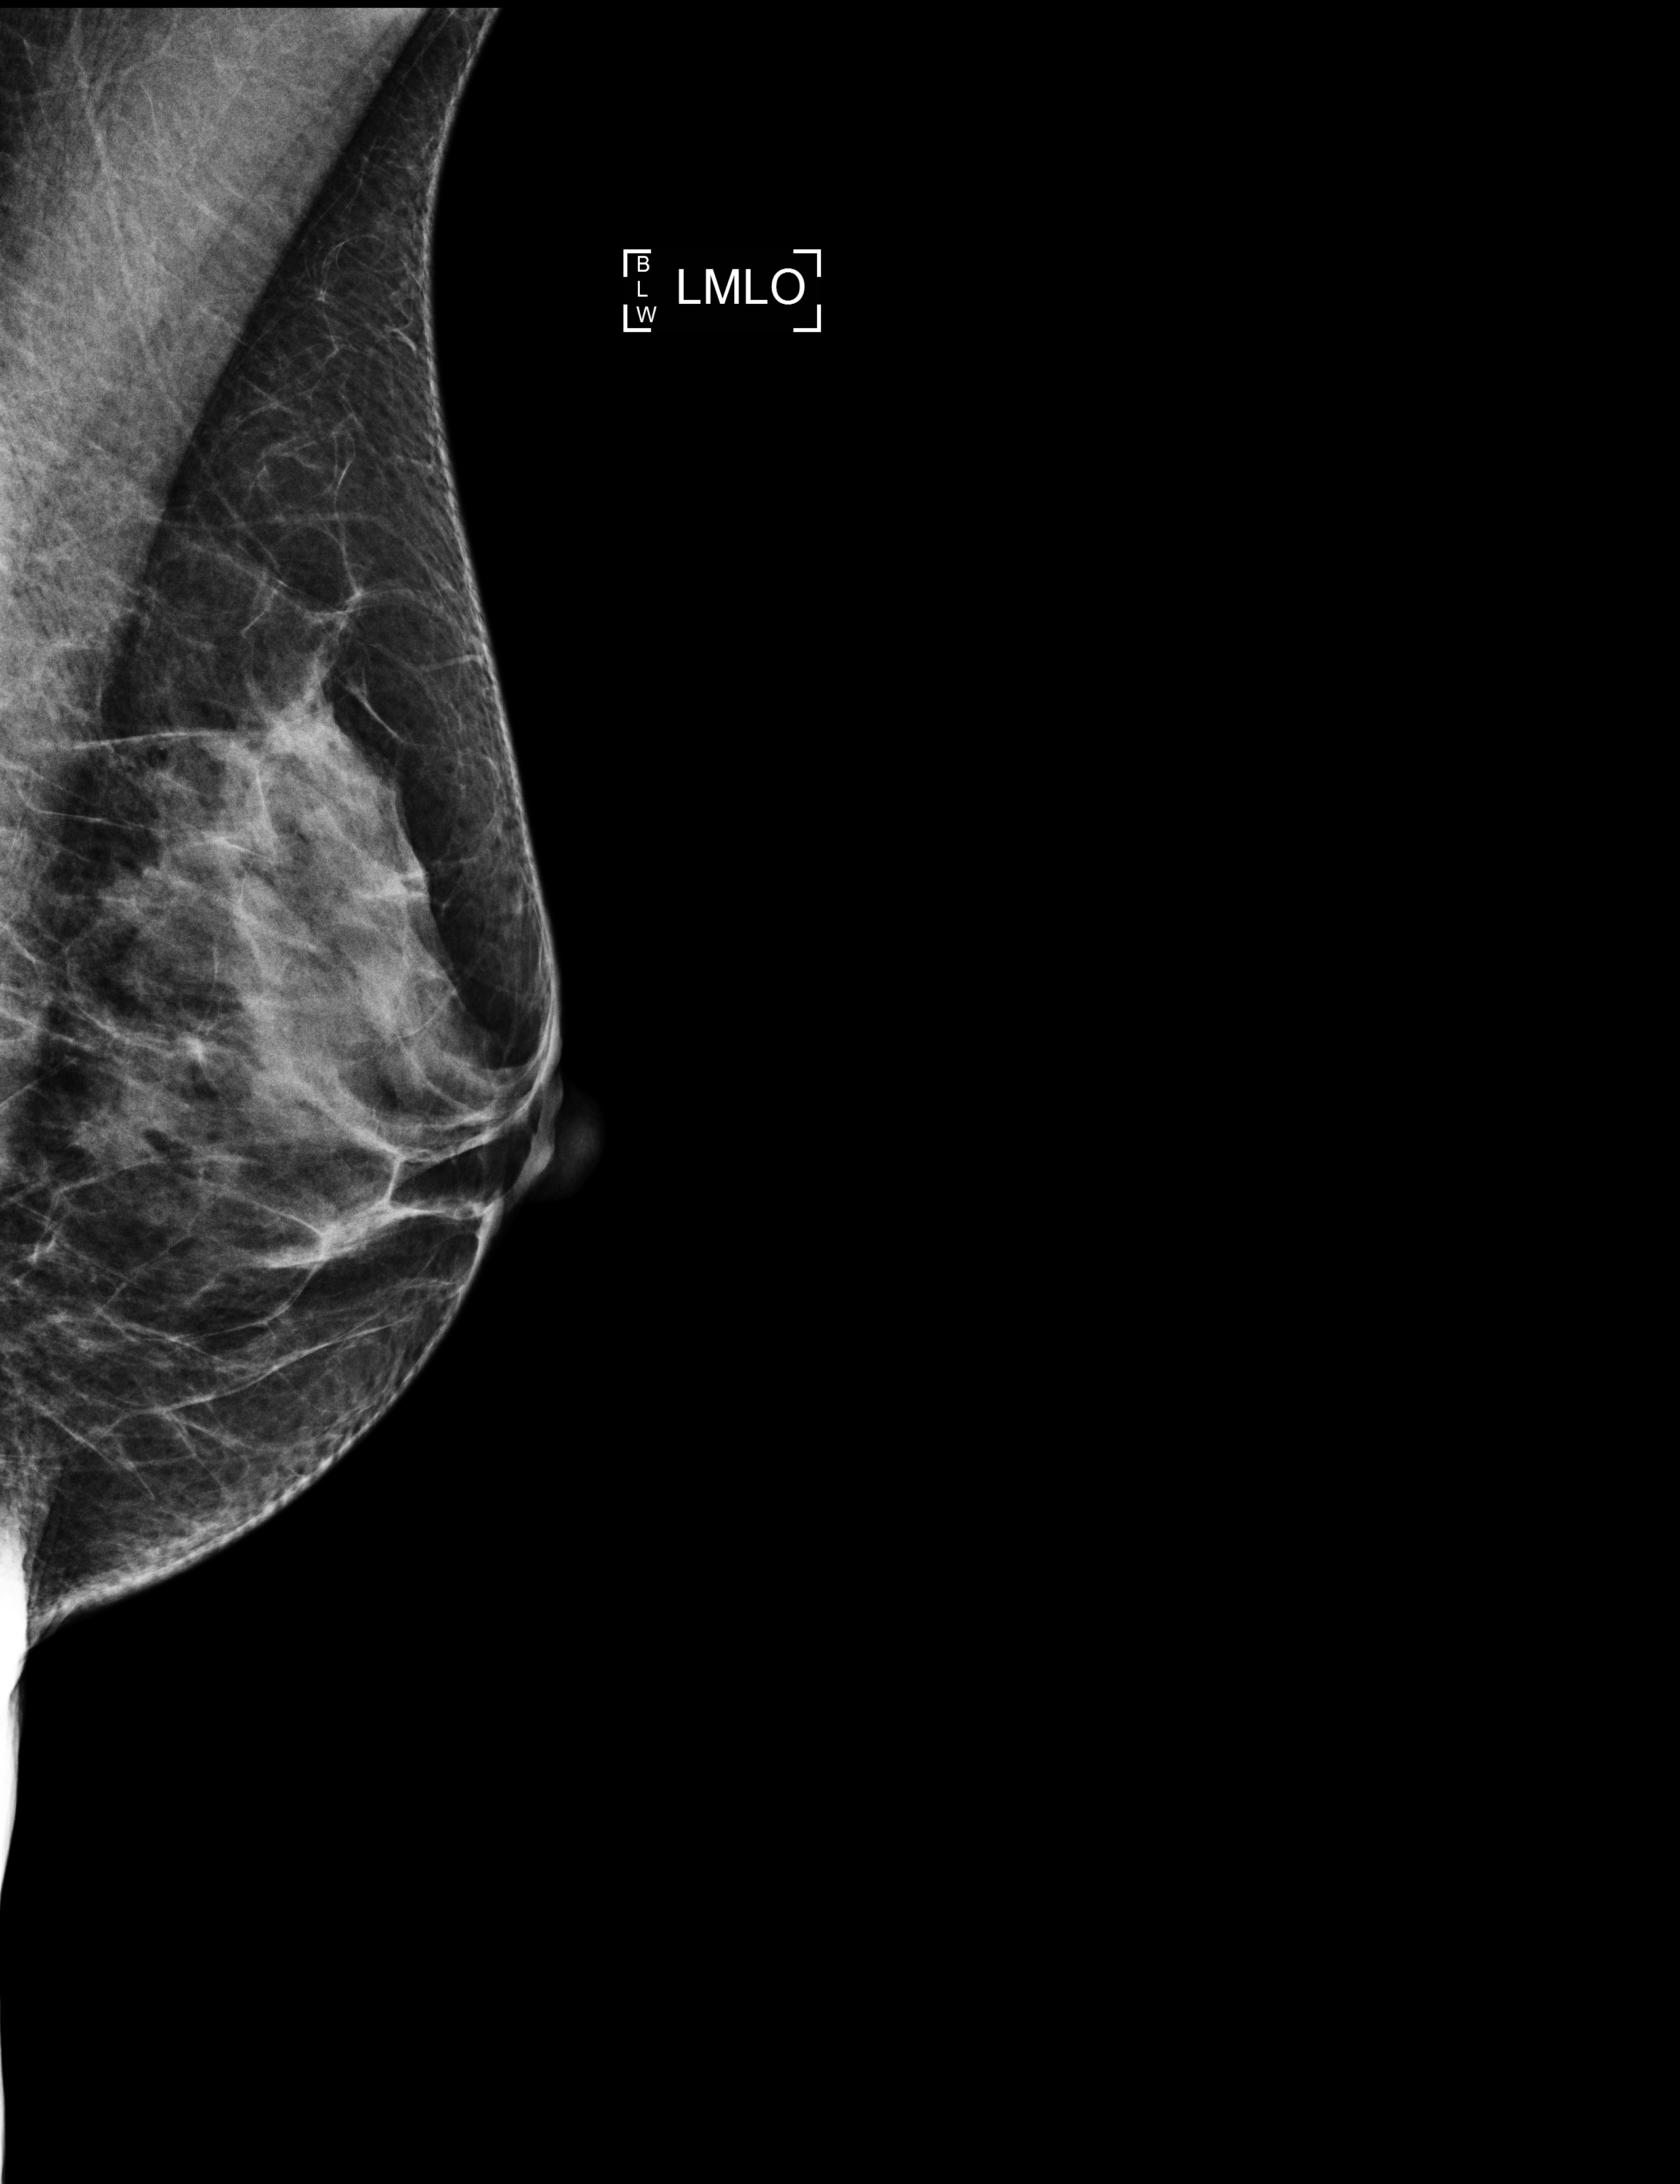
Screening examination; compressed breast thickness 40 mm; system: Selenia Dimensions. Patient aged 58 years (female).
Image type: full-field digital mammogram. Breast: left. Projection: MLO view.